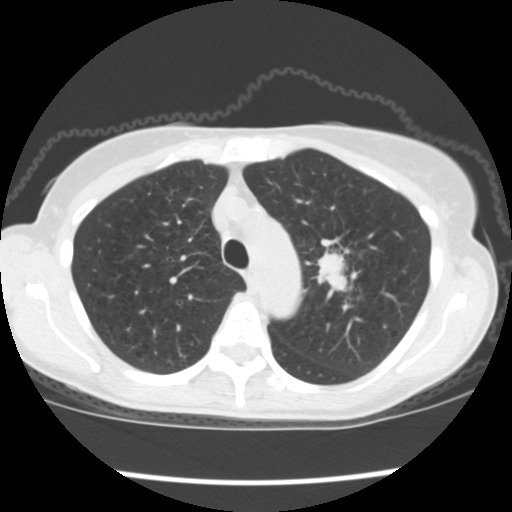
Axial slice from a low-dose chest CT screening exam. Baseline screening round. Lung window (W 1500 / L -600 HU). 2.5 mm slice thickness. Female participant, aged 67 years at enrolment.
Expert reader's lesion annotation, bounding box <307,234,380,311> (left, top, right, bottom; pixels). The exam's reader record, not a measurement of the box and not confirmed to be the same lesion: non-calcified nodule or mass ≥4 mm, left upper lobe, 34 × 32 mm, spiculated (stellate) margins, soft tissue attenuation, pre-existing on the prior screen: no. Participant outcome: lung cancer diagnosed 17 days after this screen — small cell carcinoma, NOS, left upper lobe, stage IIIA (AJCC 6th edition), 40 mm at pathology.